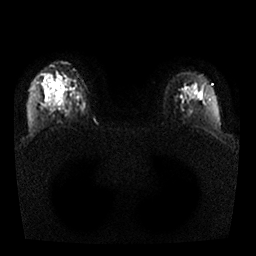
Breast MRI, one axial slice. Position 18 of 25 along the scan axis. Diffusion-weighted series; image 2 of 4 stored at this slice position (different b-values; order by instance number). 1.5 T. 4 mm slice thickness. 256 × 256 image matrix, field of view 350 × 350 mm. Female patient.
Outlined on this slice (manually delineated by an expert):
- tumour on diffusion-weighted imaging: bounding box (x1, y1, x2, y2) in pixels: (48, 93, 56, 103)